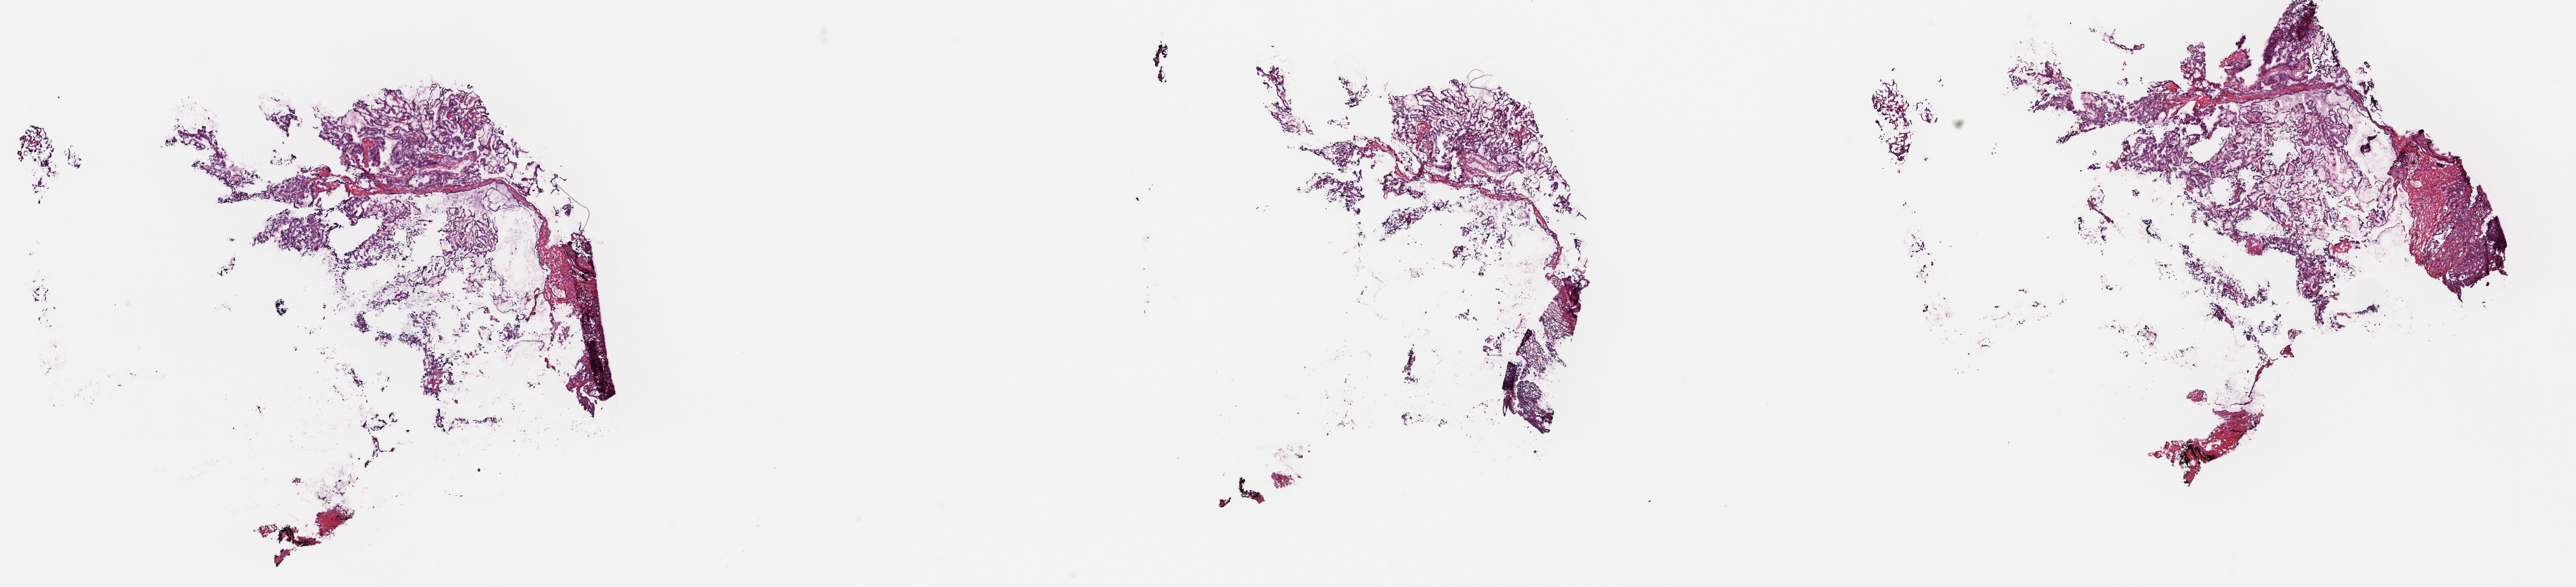
H&E whole-slide image, low-resolution overview of the scanned area, about 32.0 x 7.3 mm, frozen section from the top of the tissue portion, primary tumour sample from the thyroid. Female patient; age at initial diagnosis 26 years. Composition of this section per pathologist review: tumour cells 90%, tumour nuclei 85%.
Diagnosis: Papillary adenocarcinoma, NOS (thyroid gland).